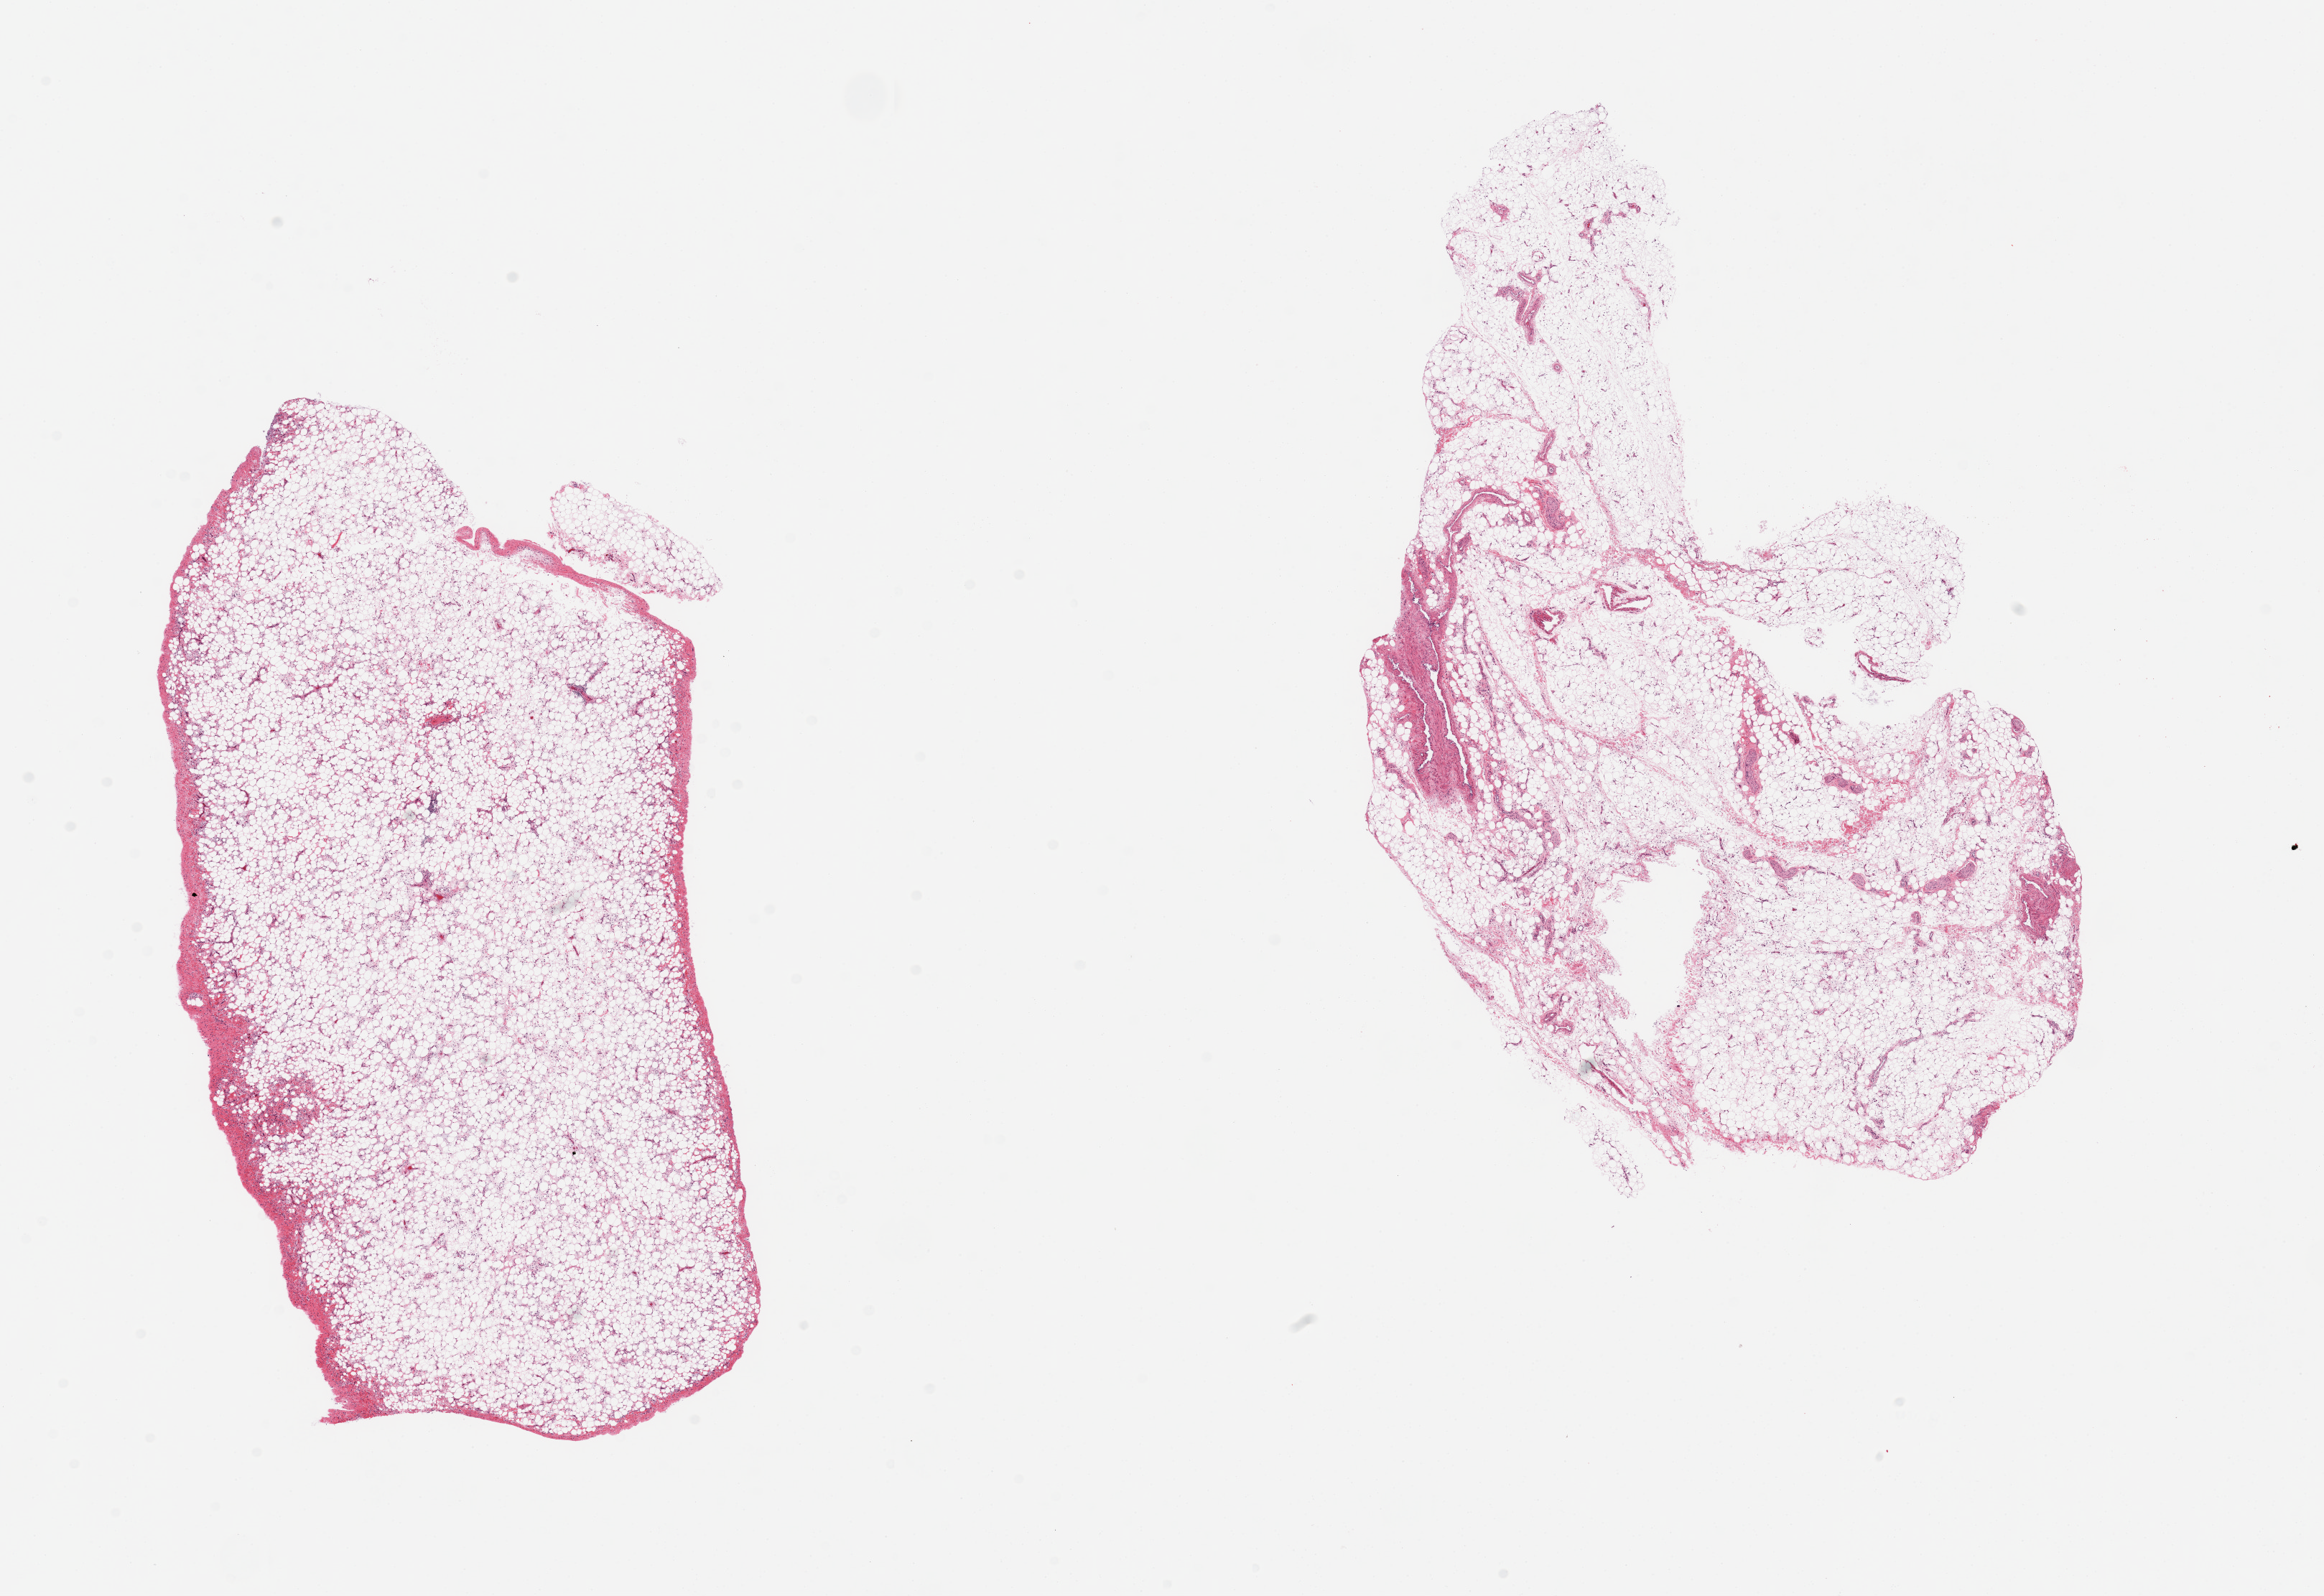
Whole-slide image, hematoxylin and eosin (H&E) stain, shown as a low-resolution overview of the whole scanned area (about 25.6 x 17.6 mm, from a 20x scan). PAXgene-fixed paraffin-embedded (PFPE) section. Section of omentum (target tissue). Tissue donor sample. Donor: male.
Reviewer comment on this tissue sample: 2 pieces, prominent mesothelial fibrosis/hyperplasia.